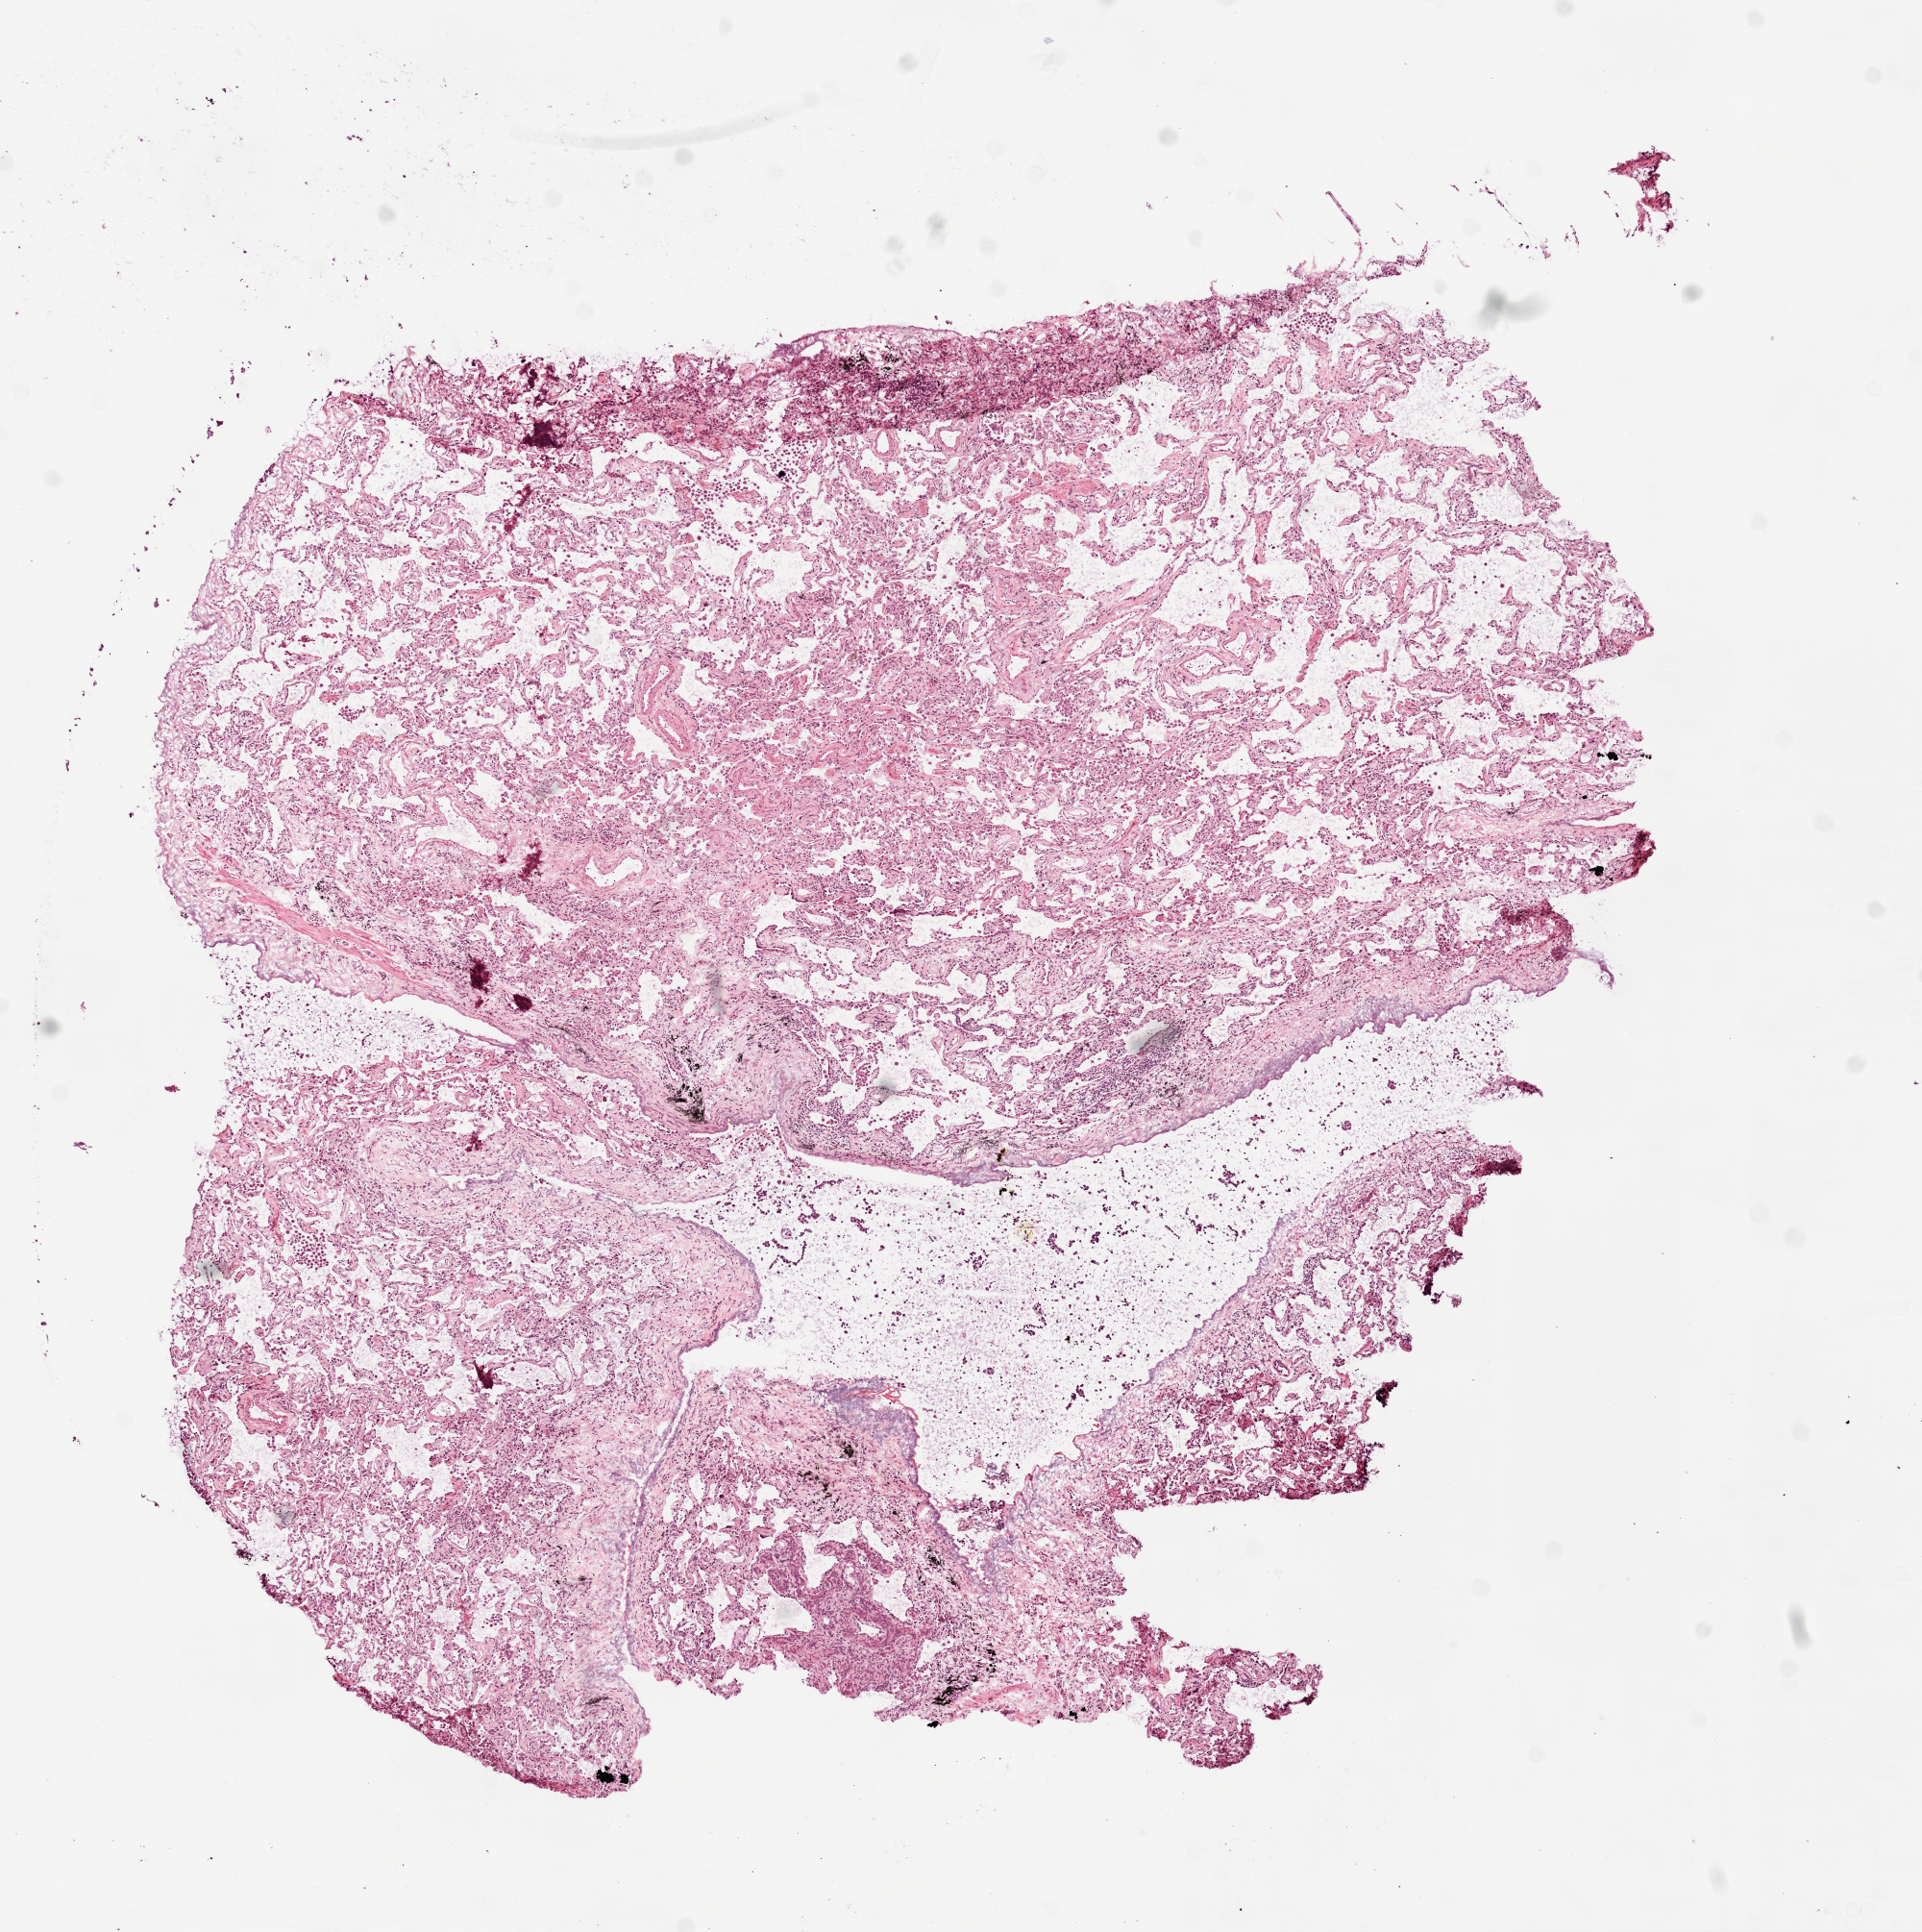
Whole-slide histology image, Hematoxylin and eosin (H&E) stained, low-resolution overview of the scanned area, about 8.0 x 8.1 mm; frozen section from the top of the tissue portion; solid tissue normal (non-tumour tissue) sample from the lung. Patient: female, age at initial diagnosis 66 years.
This section: solid tissue normal (non-tumour) sample from the same patient. Patient diagnosis: Invasive micropapillary carcinoma (upper lobe, lung).